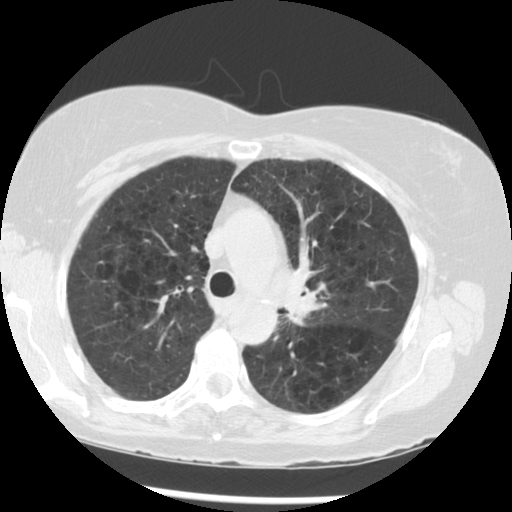
Chest CT (low-dose screening protocol), one axial image, third screening round (two years after baseline), lung window (W 1500 / L -600 HU). Female participant, aged 70 years at enrolment. Current smoker at enrolment.
Lesion marked by an expert reader, bounding box [x1, y1, x2, y2] px = [272, 259, 364, 349]. The exam's reader record, not a measurement of the box and not confirmed to be the same lesion: non-calcified nodule or mass ≥4 mm, left upper lobe, 32 × 26 mm, spiculated (stellate) margins, soft tissue attenuation, pre-existing on the prior screen: yes; interval growth: yes. Official screen result: positive, other. Participant outcome: lung cancer diagnosed 24 days after this screen — neoplasm, malignant, left upper lobe, stage IIIB (AJCC 6th edition), 40 mm at pathology.